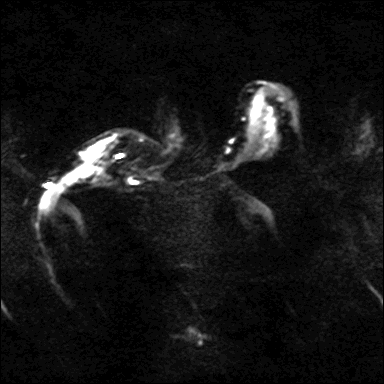
Breast MRI, one axial slice; position 26 of 40 along the scan axis; diffusion-weighted series; image 2 of 4 stored at this slice position (different b-values; order by instance number); 3 T; 4.2 mm slice thickness; 384 × 384 image matrix. Female patient.
Outlined on this slice (outlined manually by an expert reader):
- tumour on diffusion-weighted imaging: box from (x=86, y=167) to (x=95, y=175) px